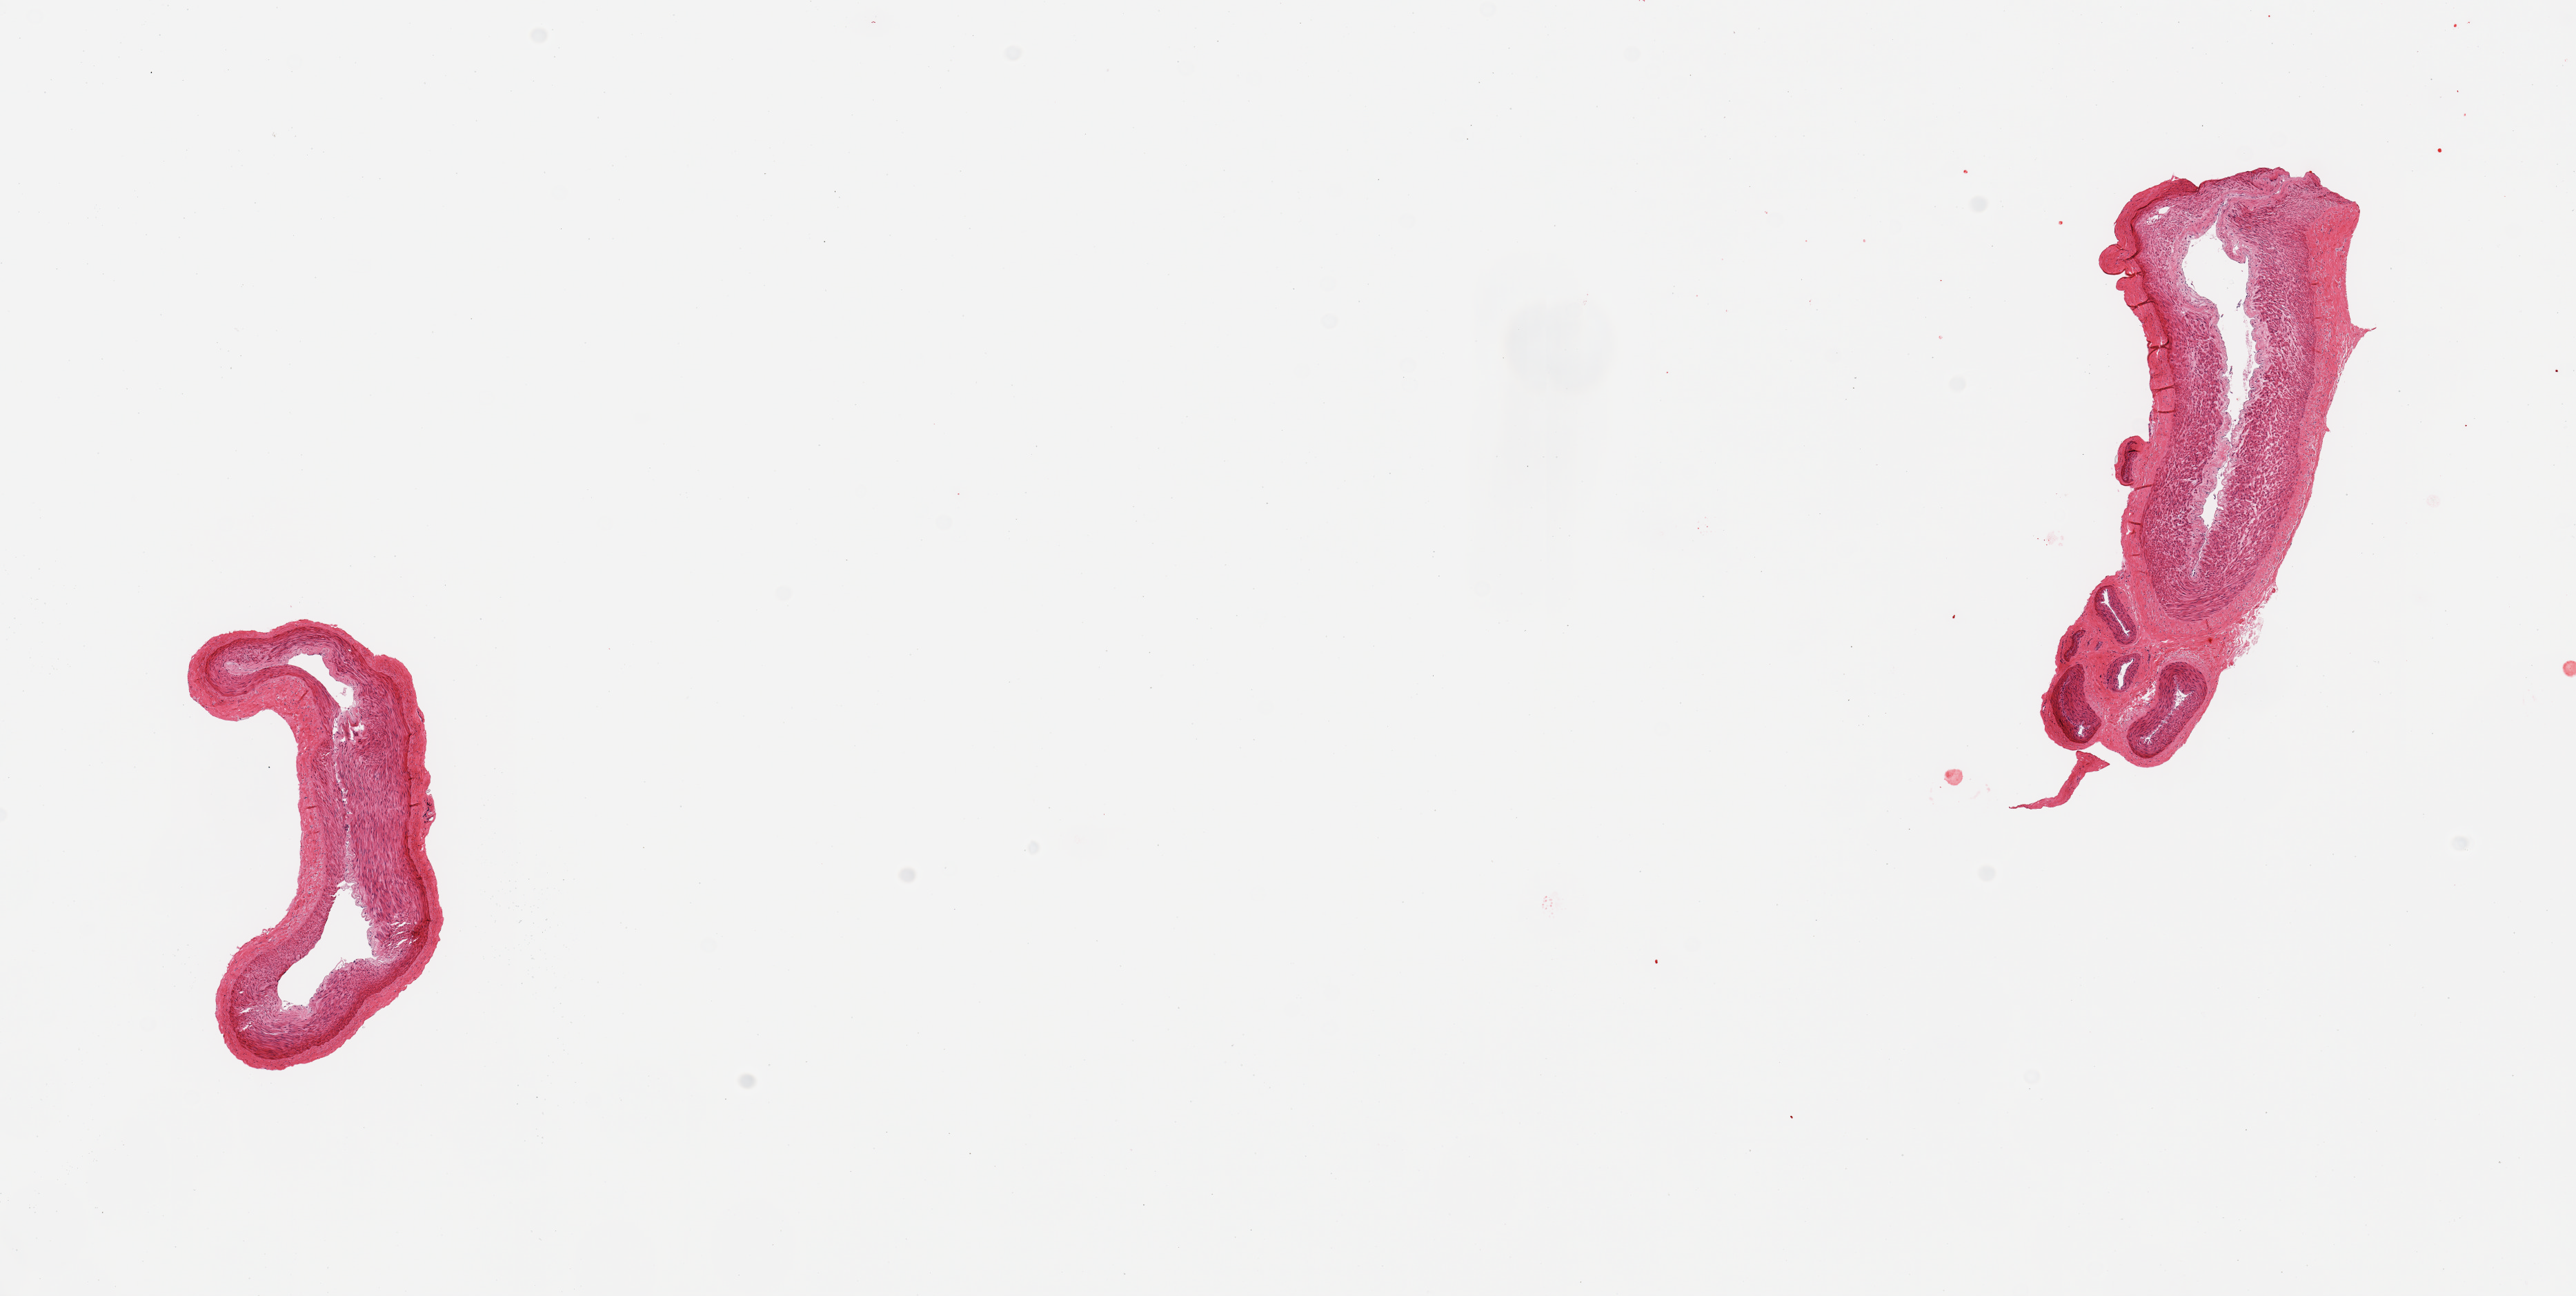
Digitized H&E-stained section, whole scanned area (about 14.8 x 7.4 mm, from a 20x scan) shown as a low-resolution overview; PAXgene-fixed, paraffin-embedded tissue; target tissue: tibial artery; donor tissue sample. Donor sex: male.
Pathologist's review note for this sample: 2 pieces.